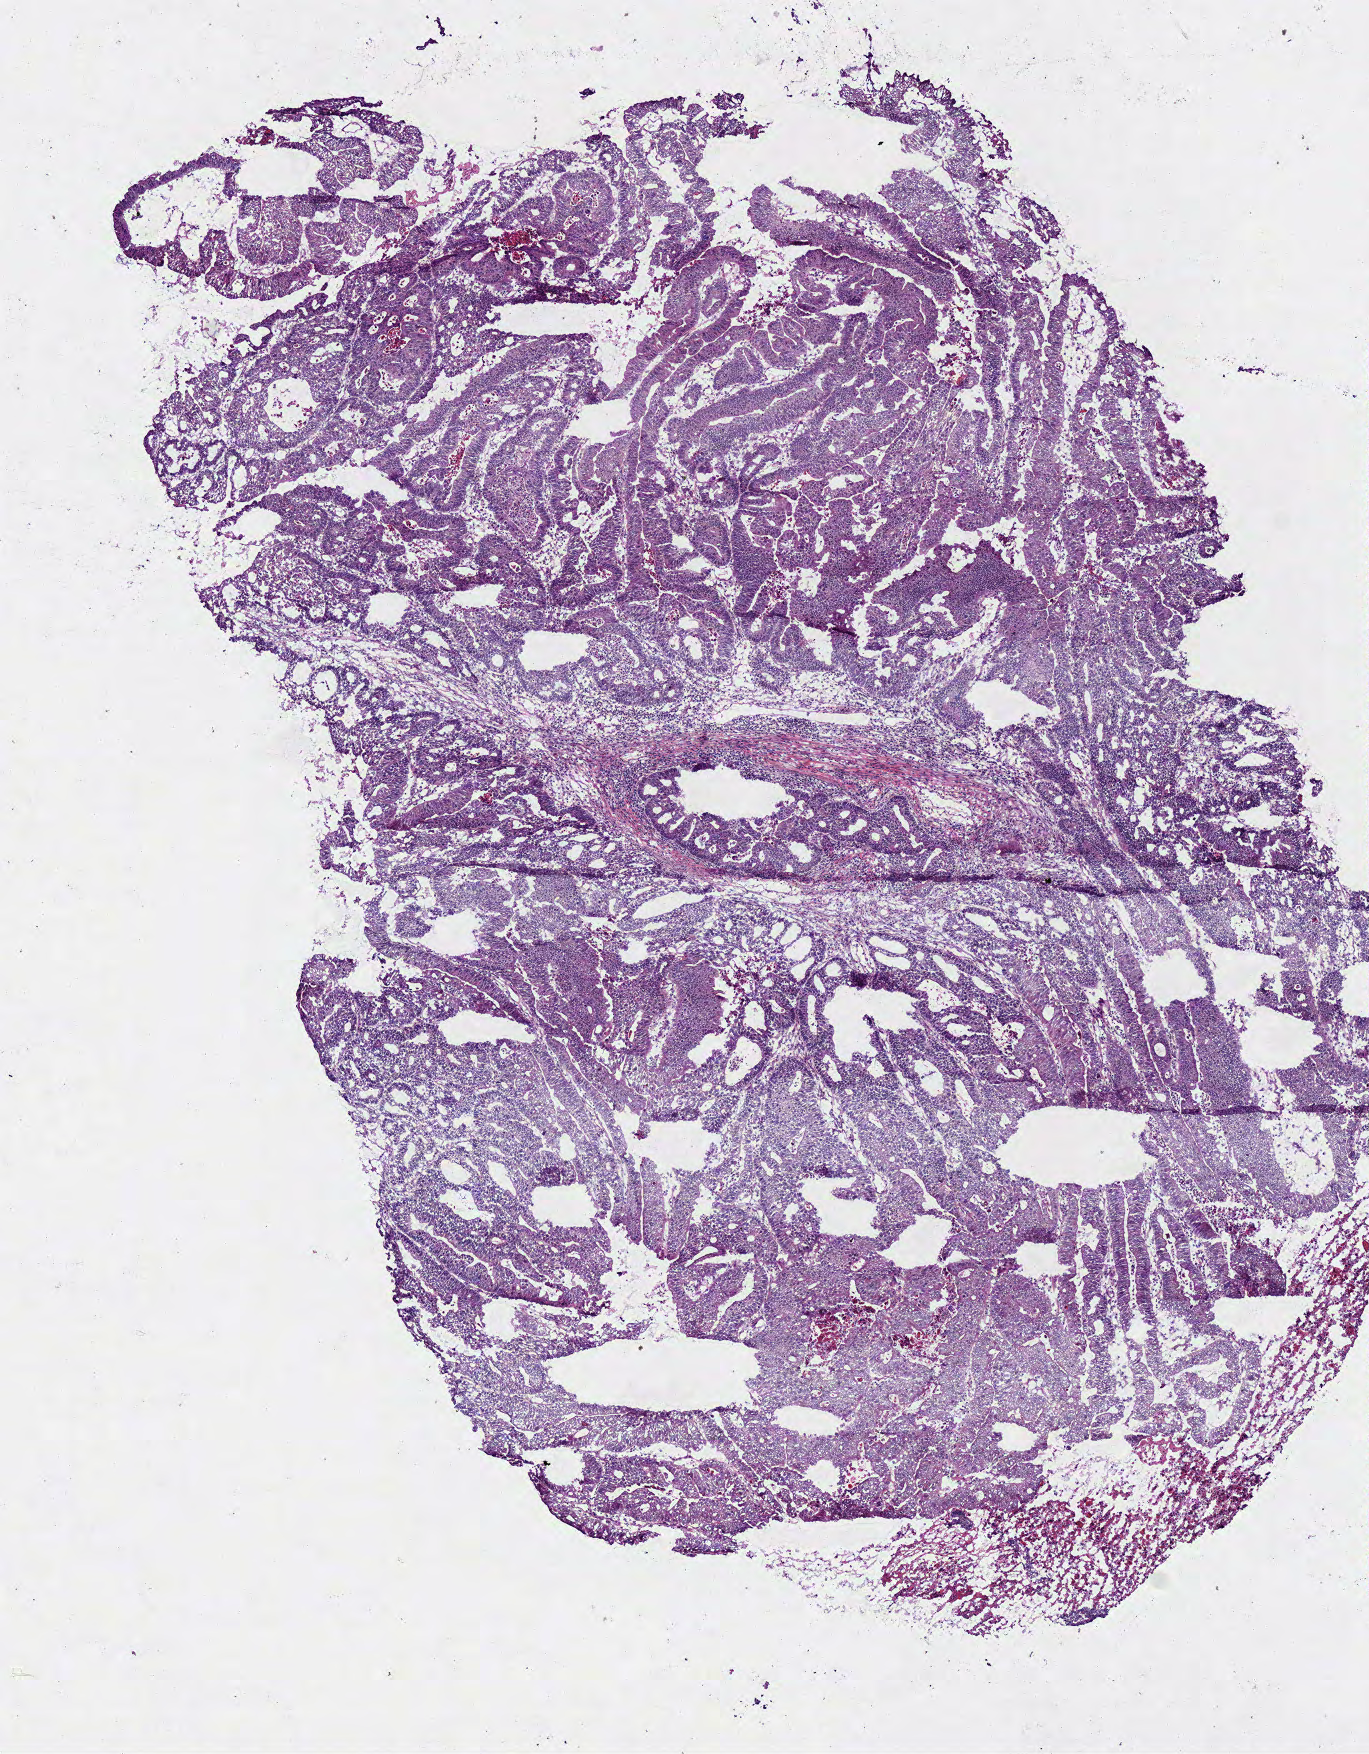
Whole-slide histology image, H&E-stained — a low-resolution overview of the entire scanned area, about 5.4 x 6.9 mm (from a 40x scan); frozen section from the bottom of the tissue portion; sample: primary tumour, colon. Female patient; age at initial diagnosis 80 years. Composition of this section per pathologist review: tumour cells 92%, tumour nuclei 80%, normal cells 0%, stromal cells 0%, necrosis 8%. Inflammatory infiltration, as recorded: lymphocyte infiltration 8%, monocyte infiltration 0%, neutrophil infiltration 8%.
• lymph nodes positive (case pathology): 1 of 6 examined
• diagnosis: Adenocarcinoma, NOS
• AJCC pathologic stage: IIIB (7th edition)